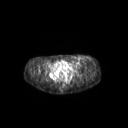
FDG PET of an extremity soft-tissue mass (from a PET/CT study), one axial slice; position 77 of 267 along the scan axis; 3.27 mm slice thickness; 128 × 128 image matrix, field of view 600 × 600 mm. Patient: female, 24 years. From the clinical record (not read from this slice): histological type: leiomyosarcoma; grade: high; site of the primary tumour: groin.
Structures marked on this image (expert contour drawn on MRI and transferred to this co-registered scan by the dataset authors):
- gross tumour volume including surrounding oedema: bounding box [x1, y1, x2, y2] px = [71, 56, 94, 64]
- gross tumour volume (mass): [77, 59, 83, 64]